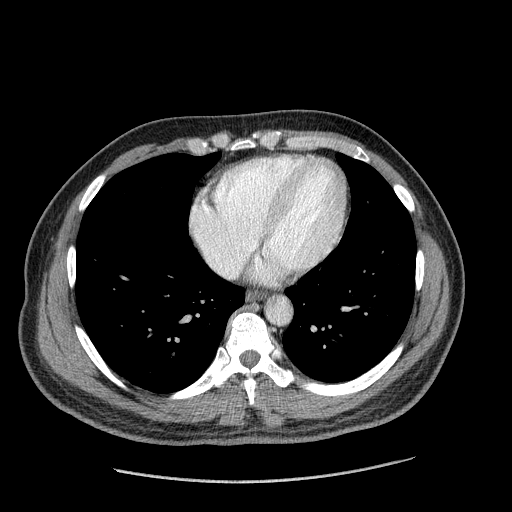
Contrast-enhanced abdominal CT (liver protocol), one axial slice; slice 179 of 182 in the series (ordered by position); 120 kVp; soft-tissue window (W 400 / L 40 HU); 2.5 mm slice thickness; 512 × 512 image matrix. From the clinical record (not read from this slice): diagnosis: hepatocellular carcinoma (patient treated with transarterial chemoembolisation; whether this scan precedes or follows treatment is not stated here); TNM stage (as recorded): Stage-I; Child-Pugh class: A; tumour differentiation: well differentiated.
Outlined on this slice (semi-automatic segmentation, software-assisted and operator-edited):
- abdominal aorta: bounding box [x1, y1, x2, y2] px = [266, 298, 291, 324]